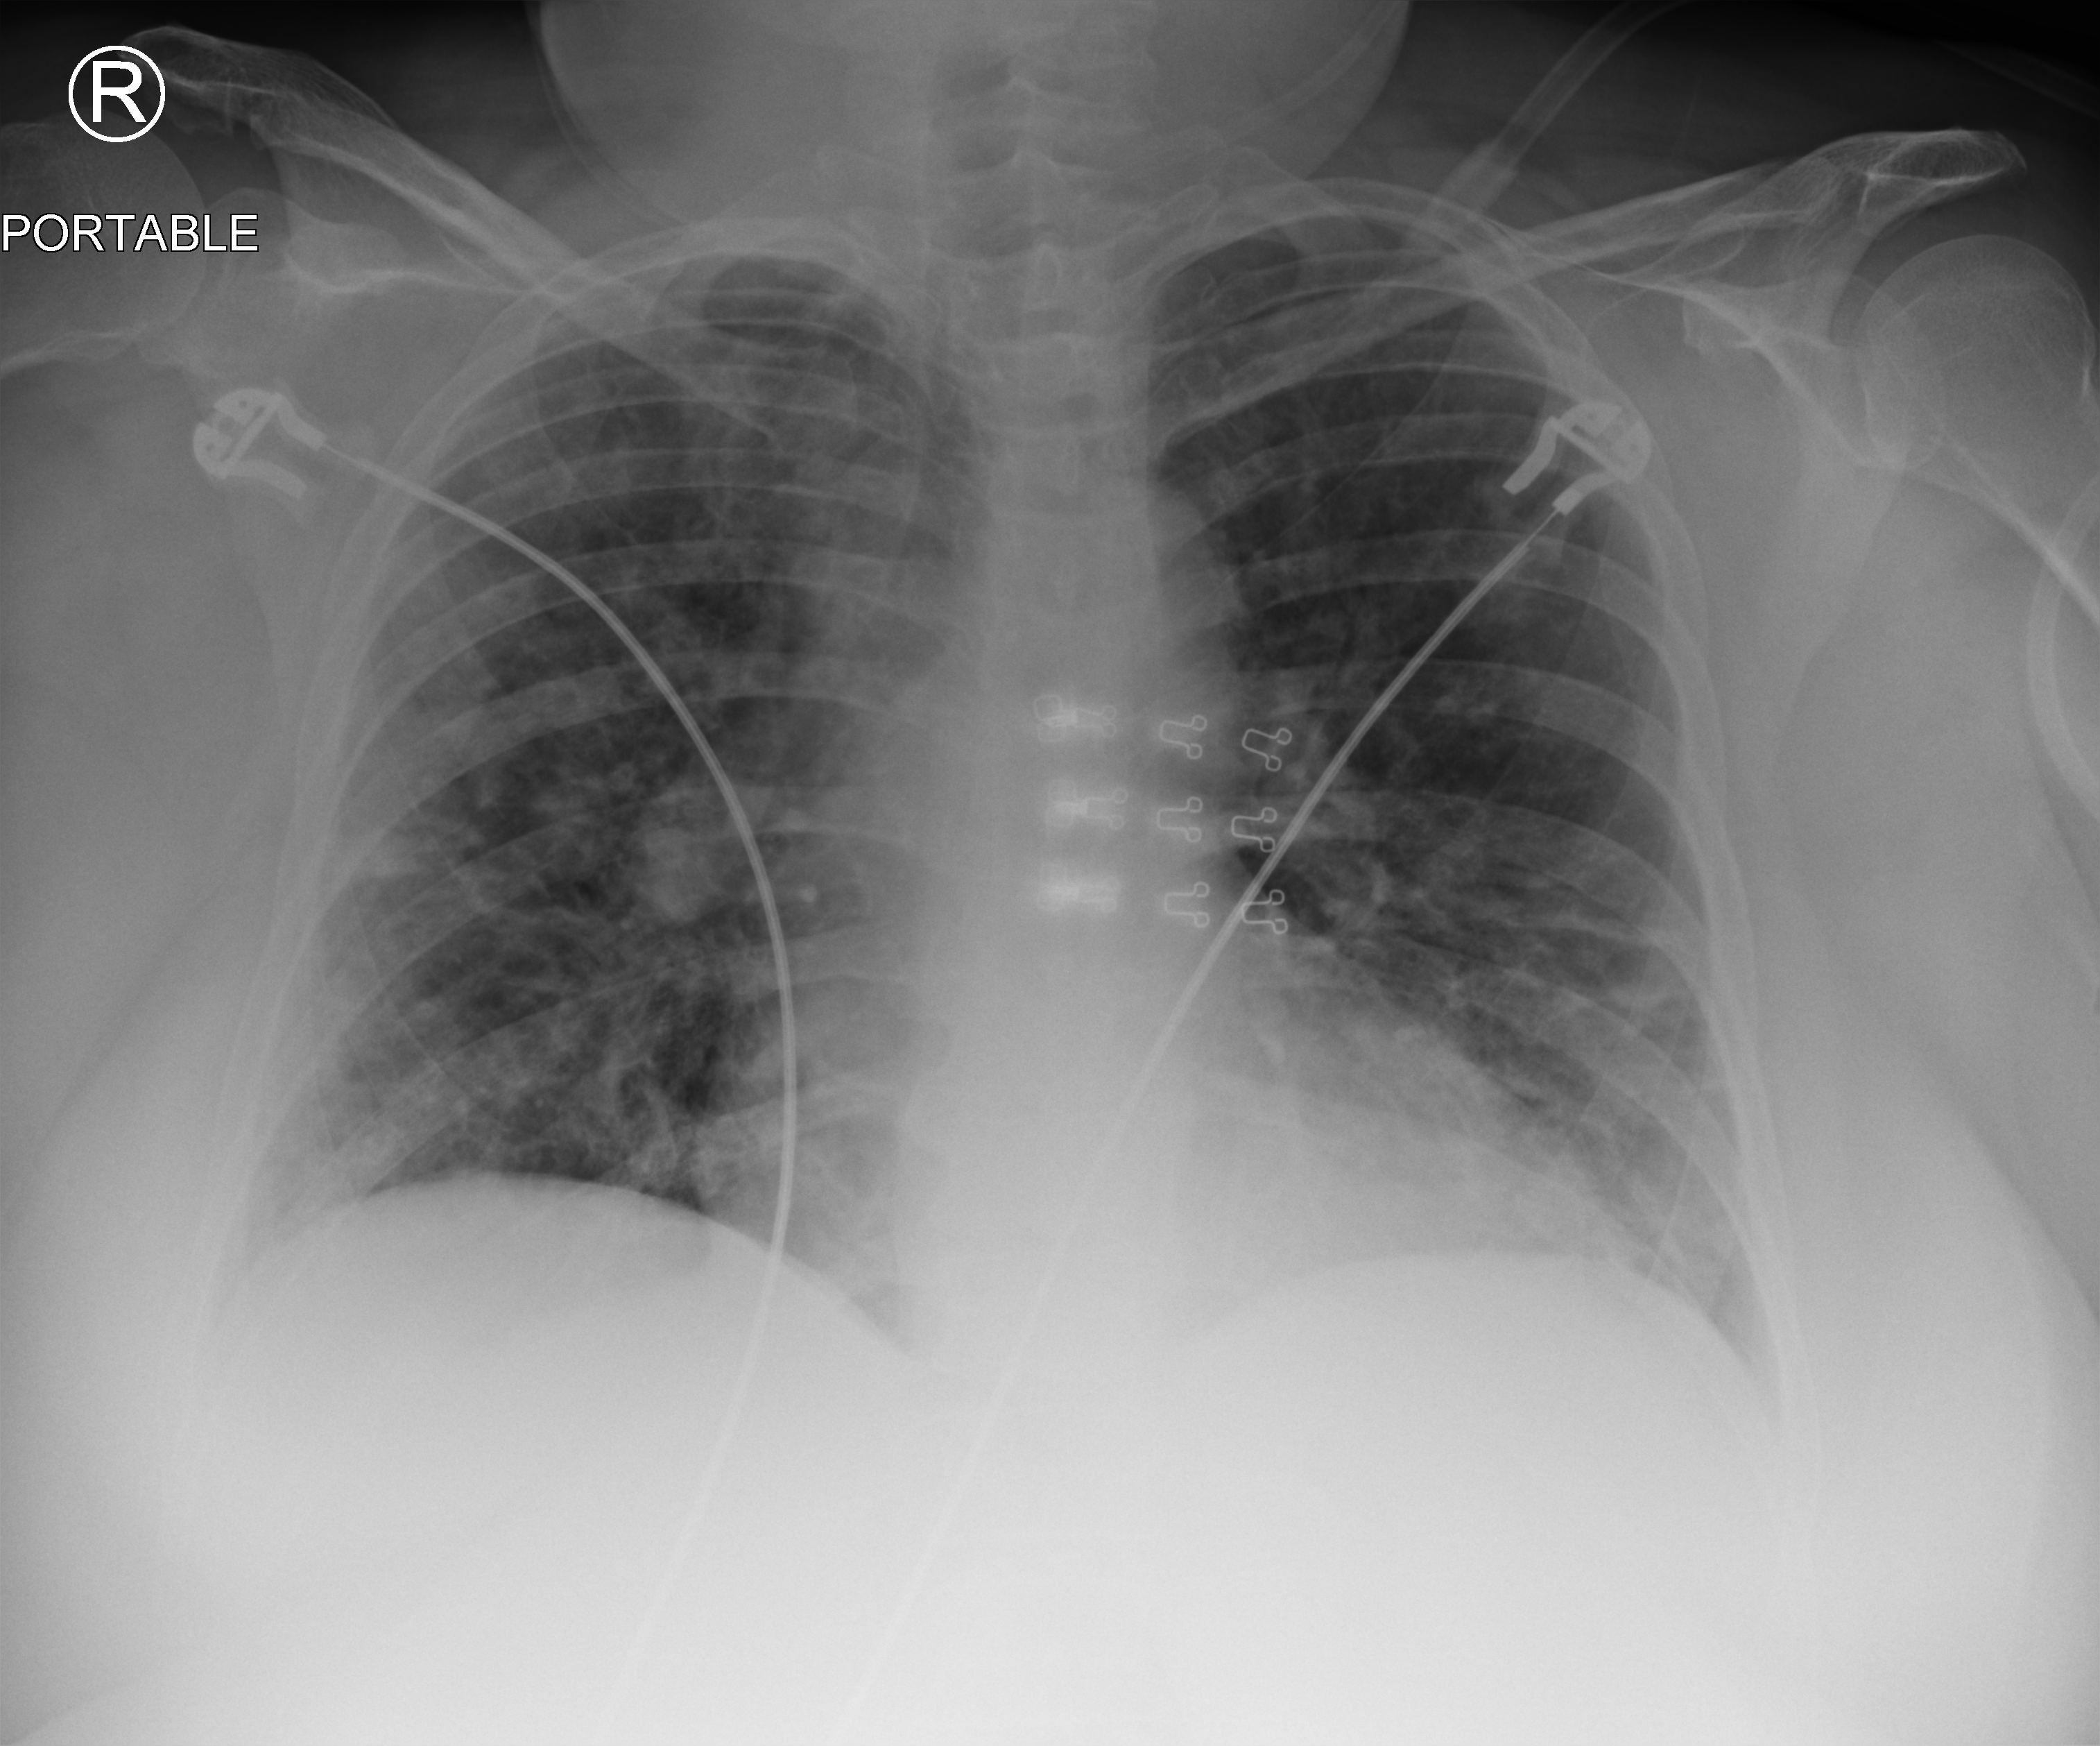
Portable chest radiograph. Patient hospitalised with COVID-19; female, aged 18–59 years.
Admission-level facts for this patient (not findings on this image; timing relative to this image not recorded): diabetes (admission record): no; admitted to intensive care during this hospital stay: no.